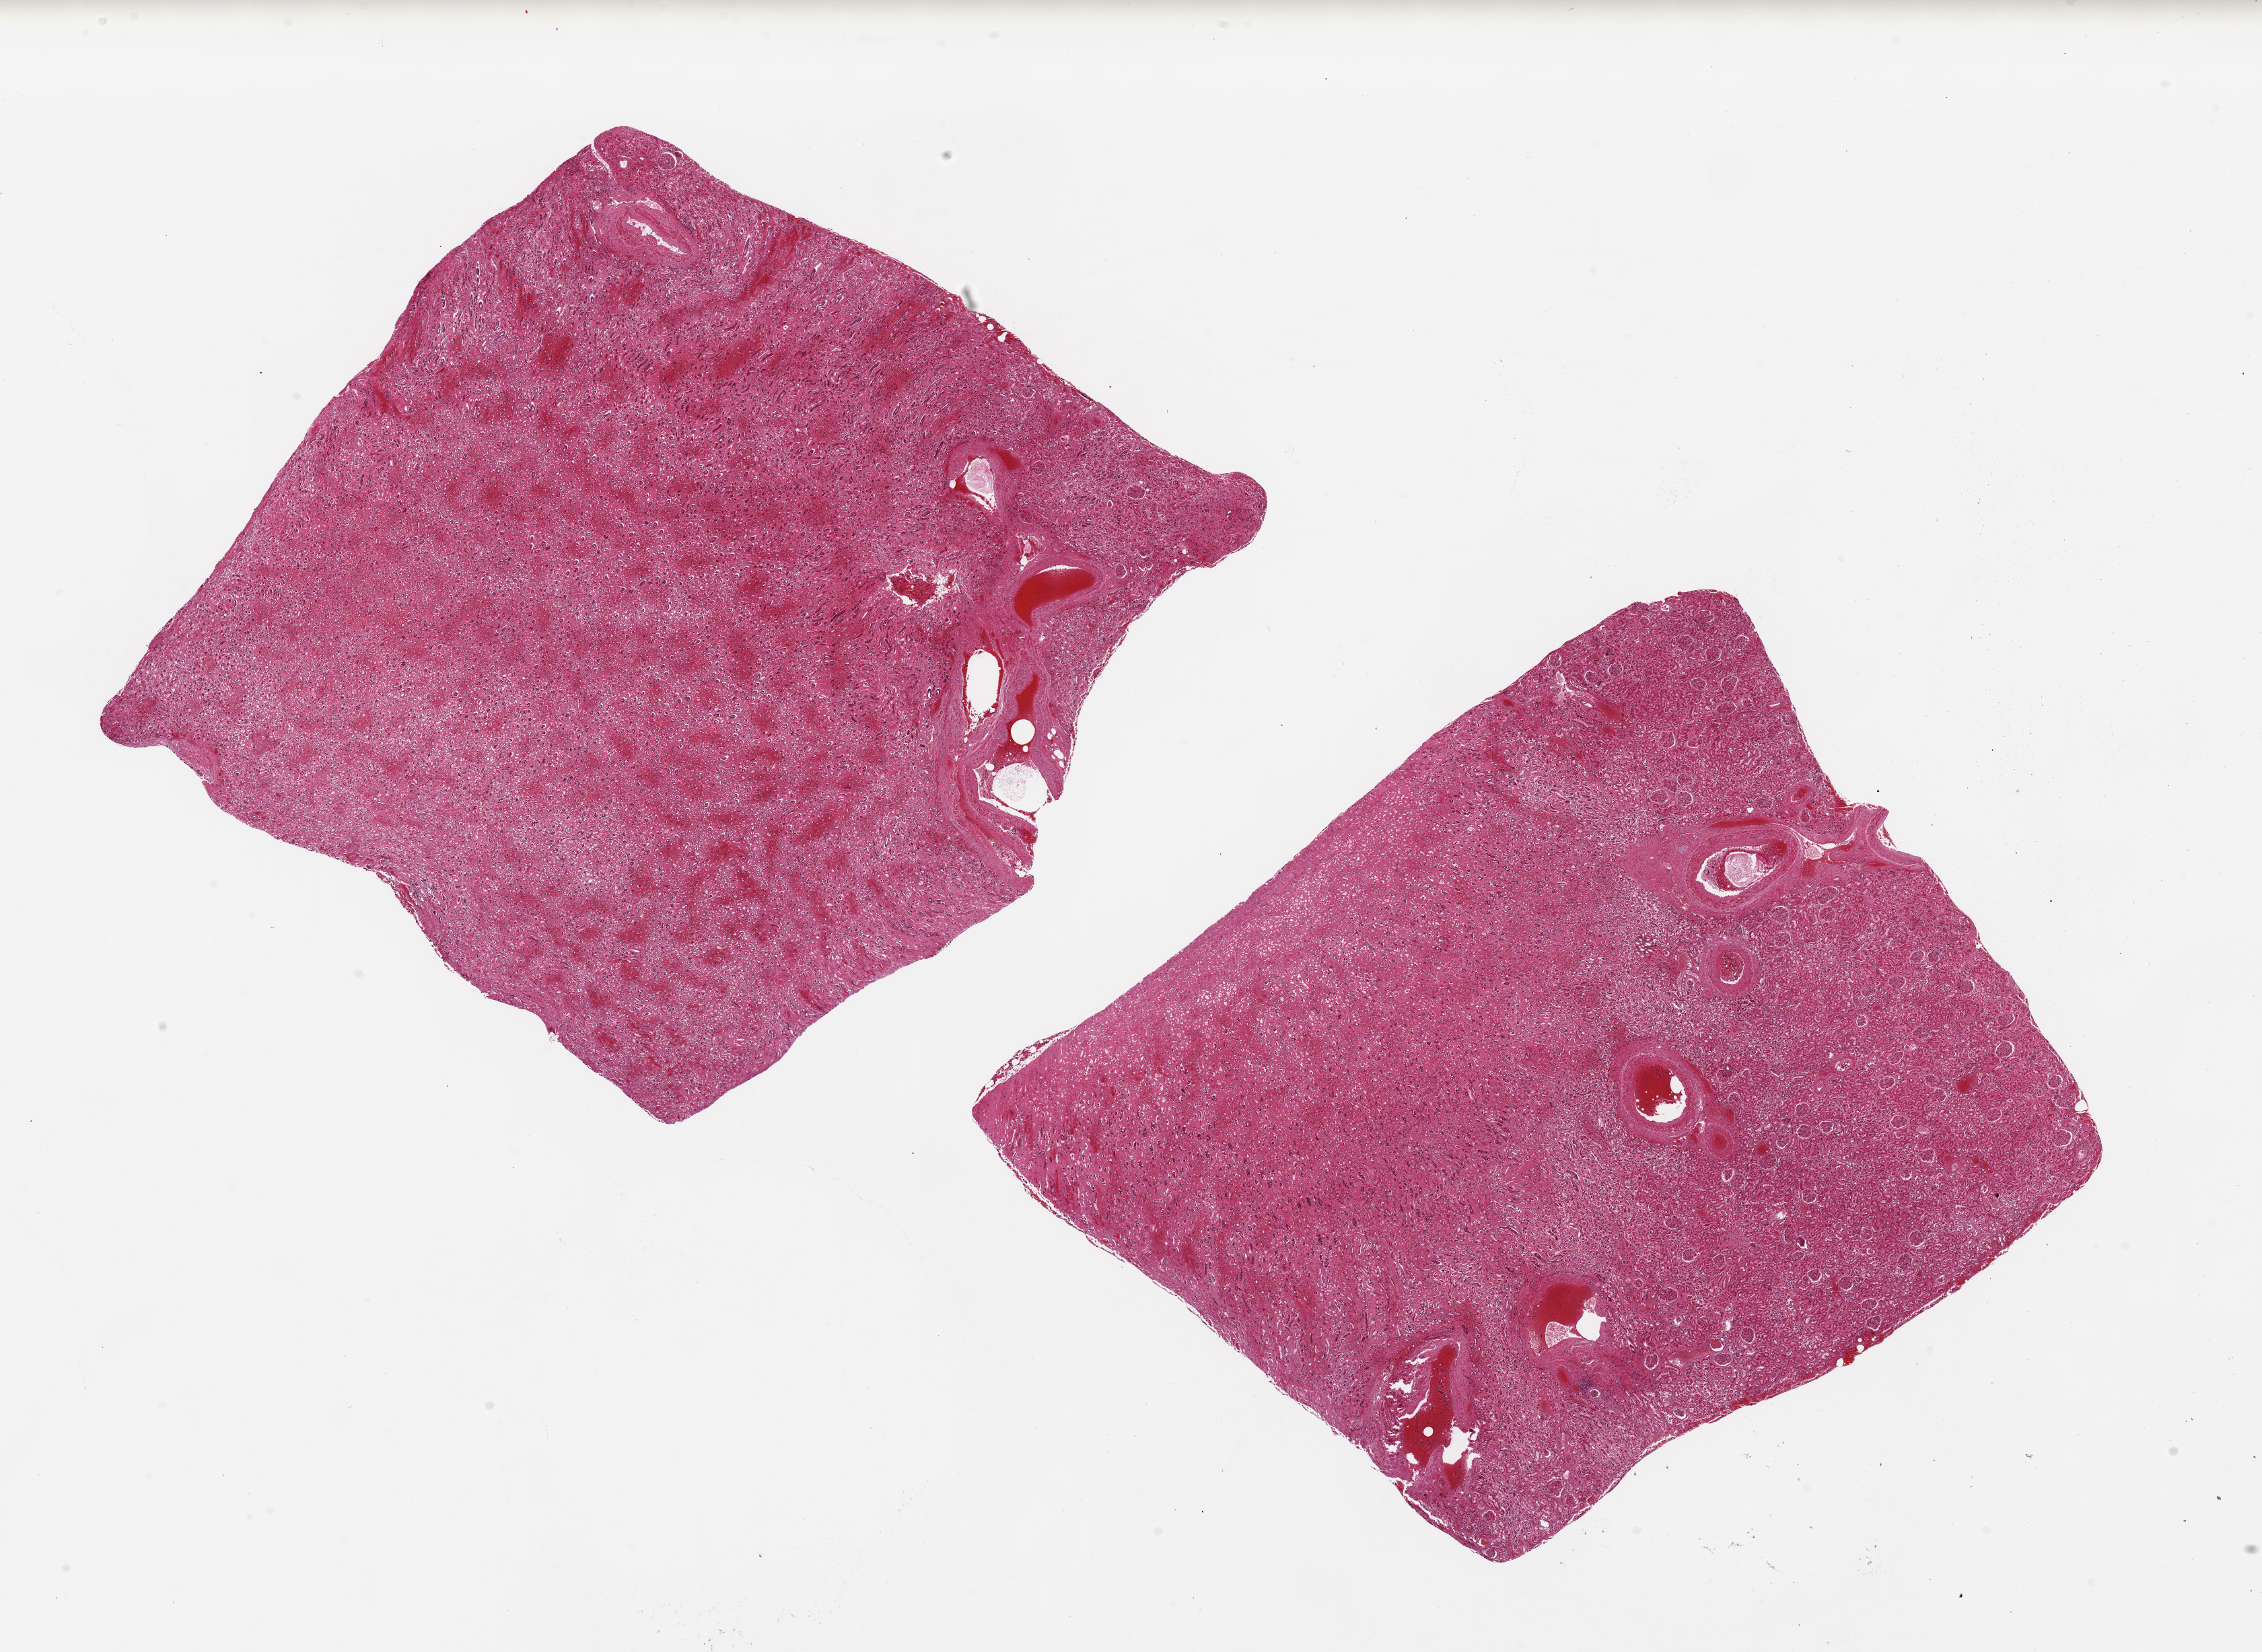
H&E whole-slide image, shown as a low-resolution overview of the whole scanned area (about 26.6 x 19.4 mm). Donor sex: male.
Specimen: PAXgene-fixed, paraffin-embedded tissue; section of renal medulla (target tissue); tissue donor sample.